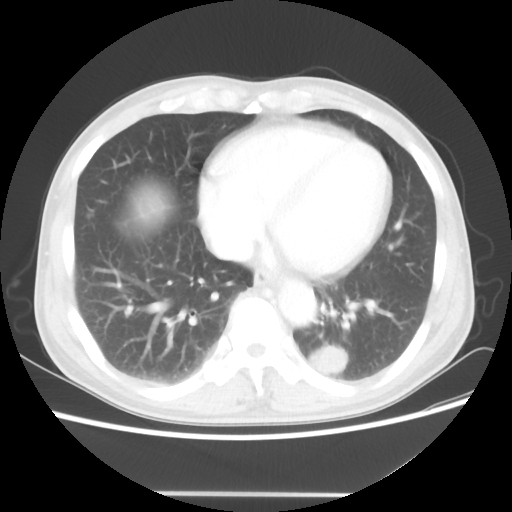
Chest CT, one axial slice. Slice 21 of 60 in the series (ordered by position). 100 kVp. Lung window (W 1500 / L -600 HU). 512 × 512 image matrix. Male patient, age 55 years. Case-level facts recorded for this patient, not image findings: clinical TNM (as recorded): T1c N3 M0.
Structures marked on this image (bounding box drawn by a radiologist):
- lung tumour (recorded histology: small cell carcinoma): box from (x=303, y=339) to (x=351, y=381) px